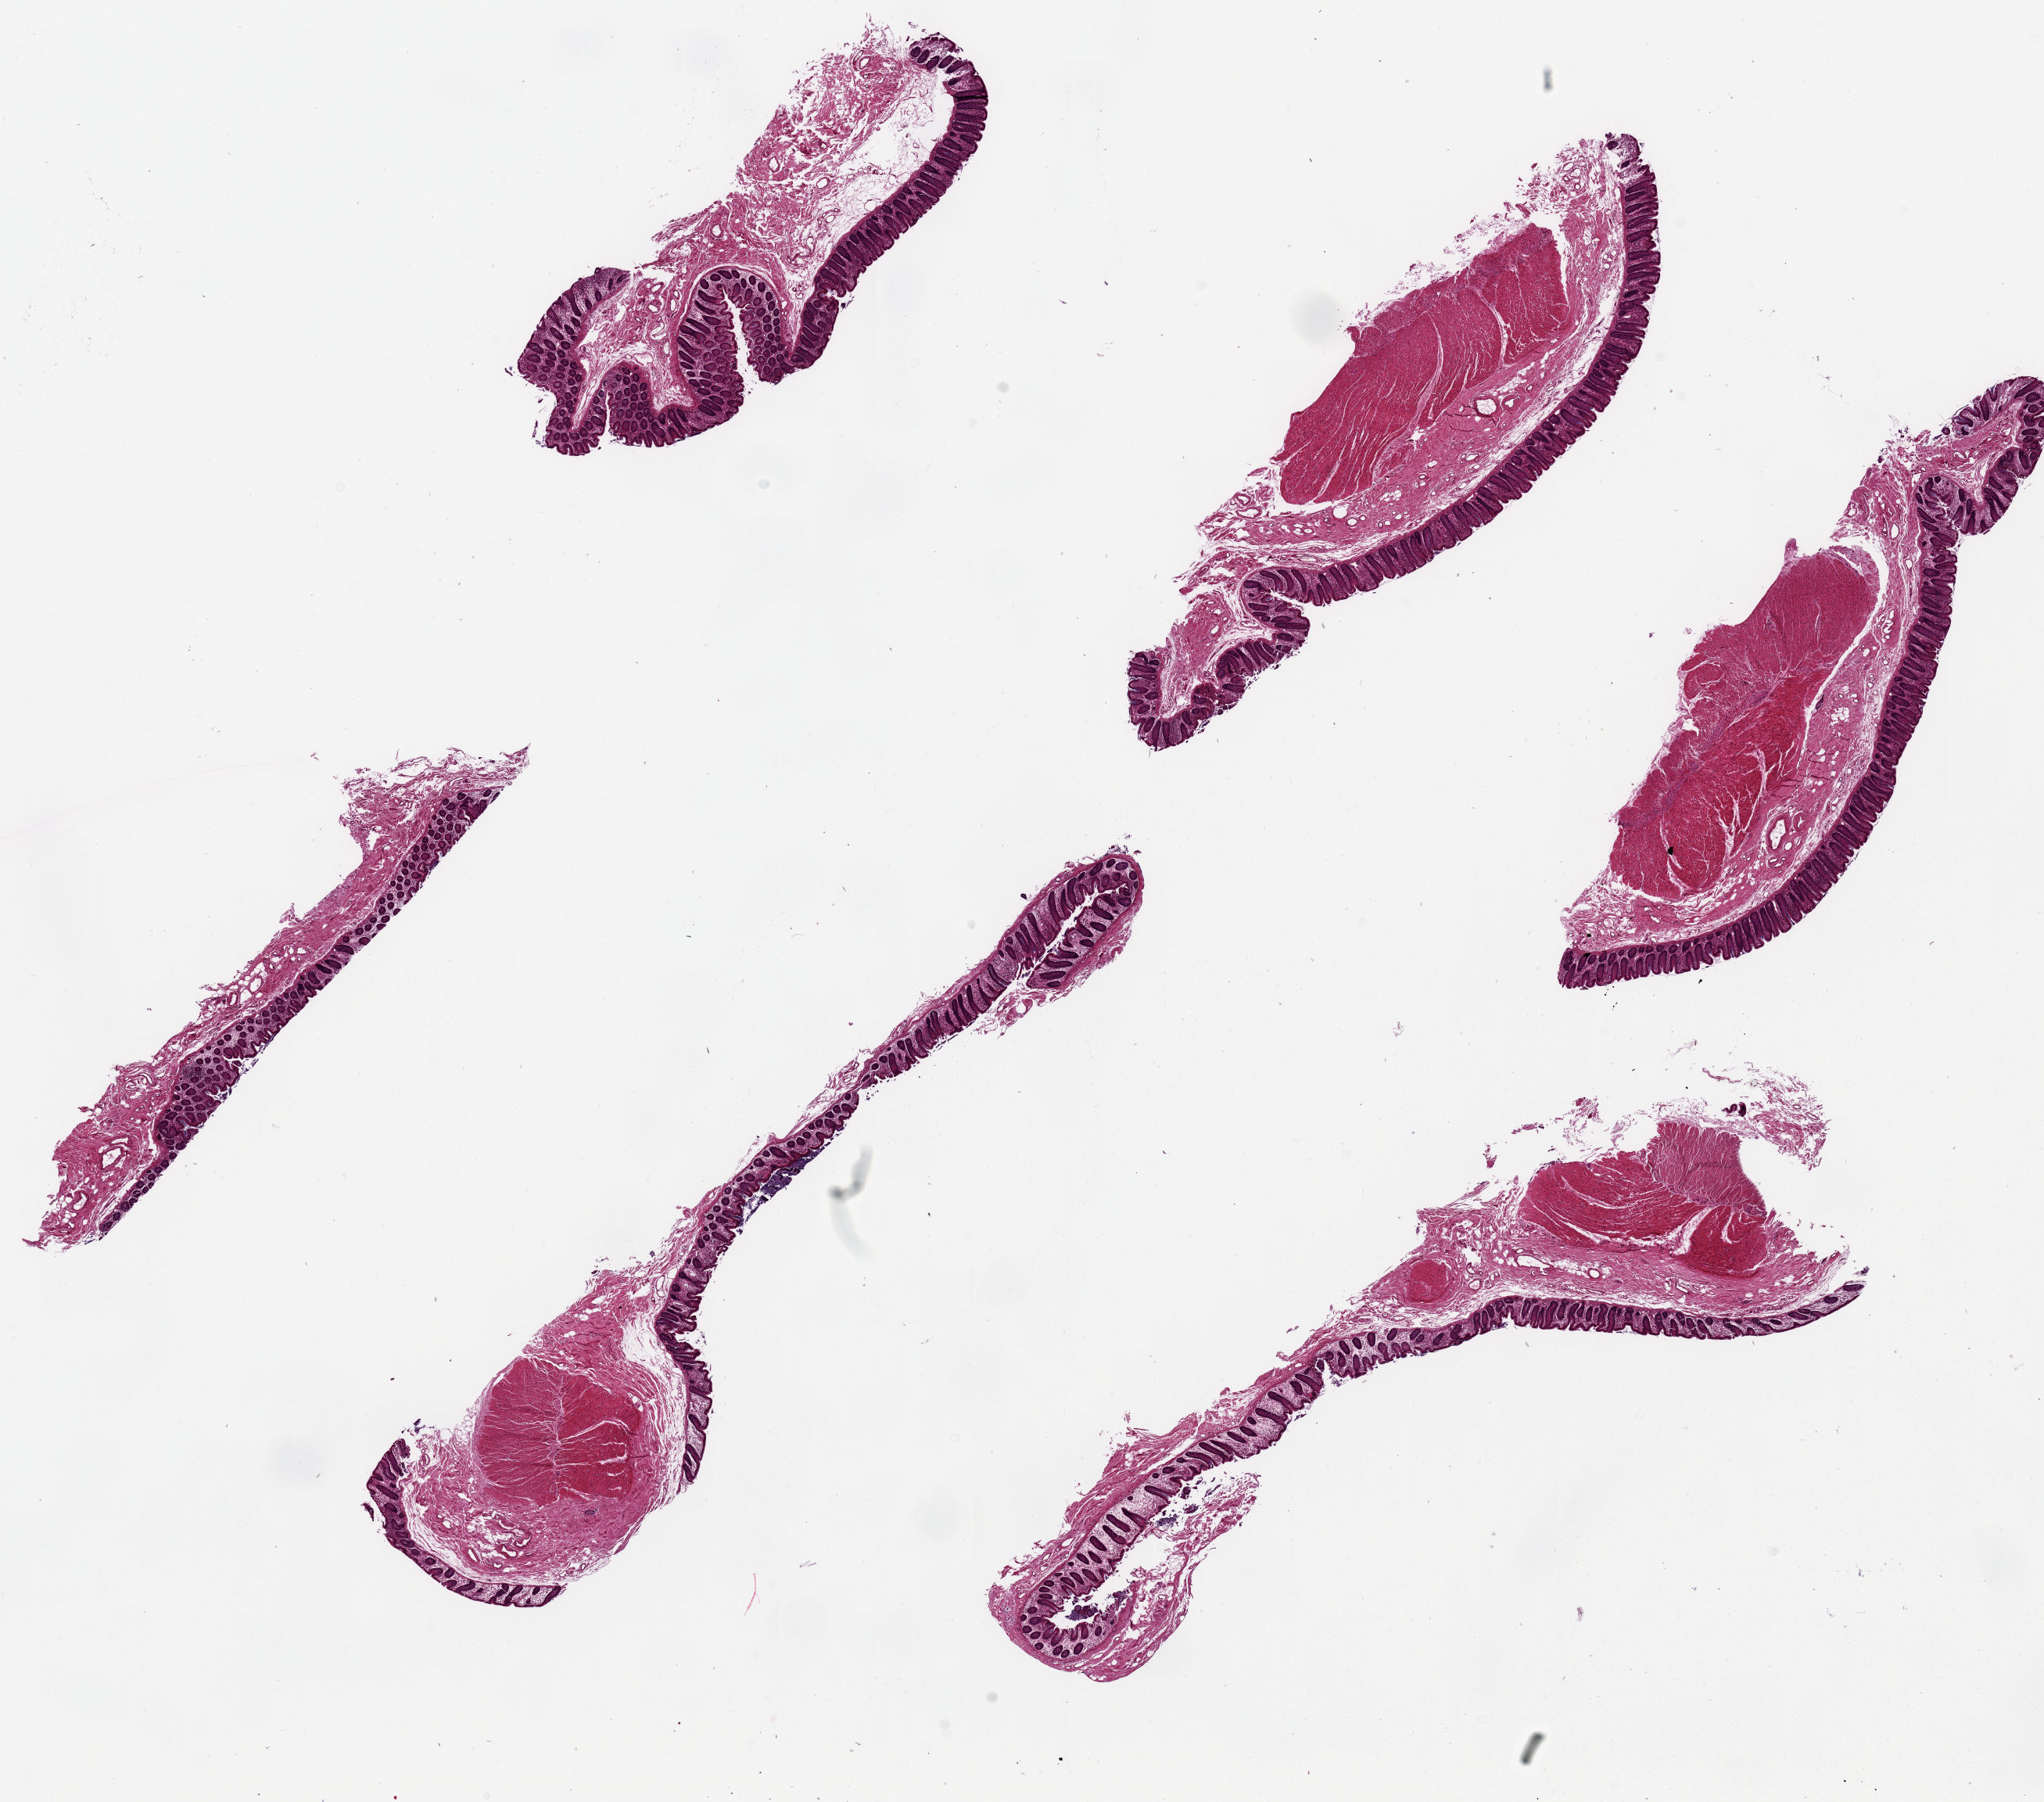
Whole-slide image, hematoxylin and eosin (H&E) stain — a low-resolution overview of the entire scanned area, about 20.7 x 18.2 mm (from a 20x scan). PAXgene-fixed paraffin-embedded (PFPE) section. Section of transverse colon (target tissue). Tissue donor sample. Female donor.
• review note (as recorded): 6 pieces, up to 10x2mm; 2 with no muscle, 2 with focal muscle